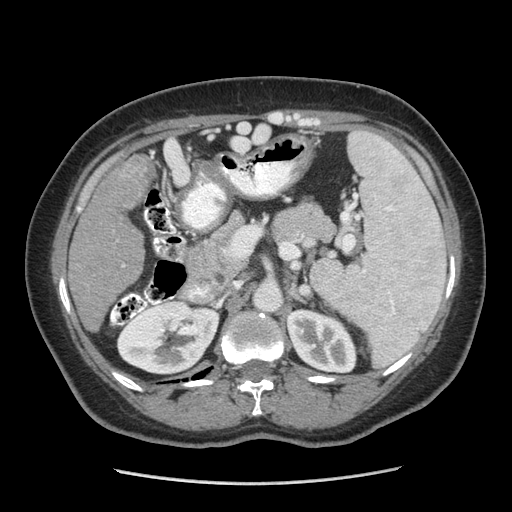
Contrast-enhanced abdominal CT (liver protocol), one axial slice. Slice 141 of 185 in the series (ordered by position). Soft-tissue window (W 400 / L 40 HU). 2.5 mm slice thickness. 512 × 512 image matrix, field of view 360 × 360 mm. Case-level facts recorded for this patient, not image findings: diagnosis: hepatocellular carcinoma (patient treated with transarterial chemoembolisation; whether this scan precedes or follows treatment is not stated here); TNM stage (as recorded): Stage-I; Child-Pugh class: A; tumour differentiation: poorly differentiated.
Annotated regions visible in this slice (semi-automatic segmentation, software-assisted and operator-edited):
- liver parenchyma outside the tumour (the mass and vessels are separate outlines, so this box may not span the whole liver): bounding box [x1, y1, x2, y2] px = [68, 153, 154, 332]
- mass: [92, 157, 154, 215]